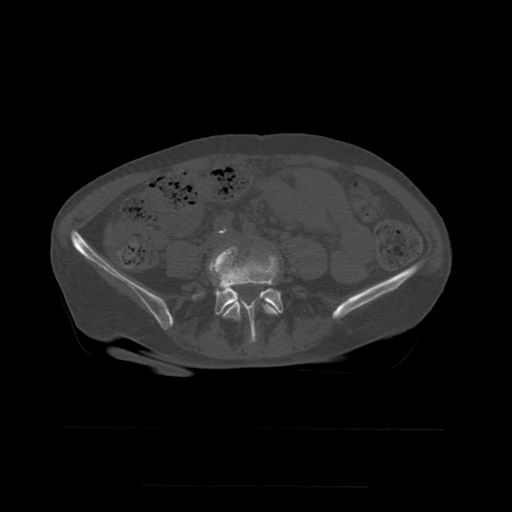
CT including the spine, one axial slice. Position 154 of 544 along the scan axis. Bone window (W 1800 / L 400 HU). 1.25 mm slice thickness. 512 × 512 image matrix. Patient age 58 years. From the clinical record (not read from this slice): primary cancer: lung.
Outlined on this slice (semi-automatically segmented with operator editing):
- L4 vertebra: bounding box <210,247,278,340> (left, top, right, bottom; pixels)
- L5 vertebra: <201,246,284,344>